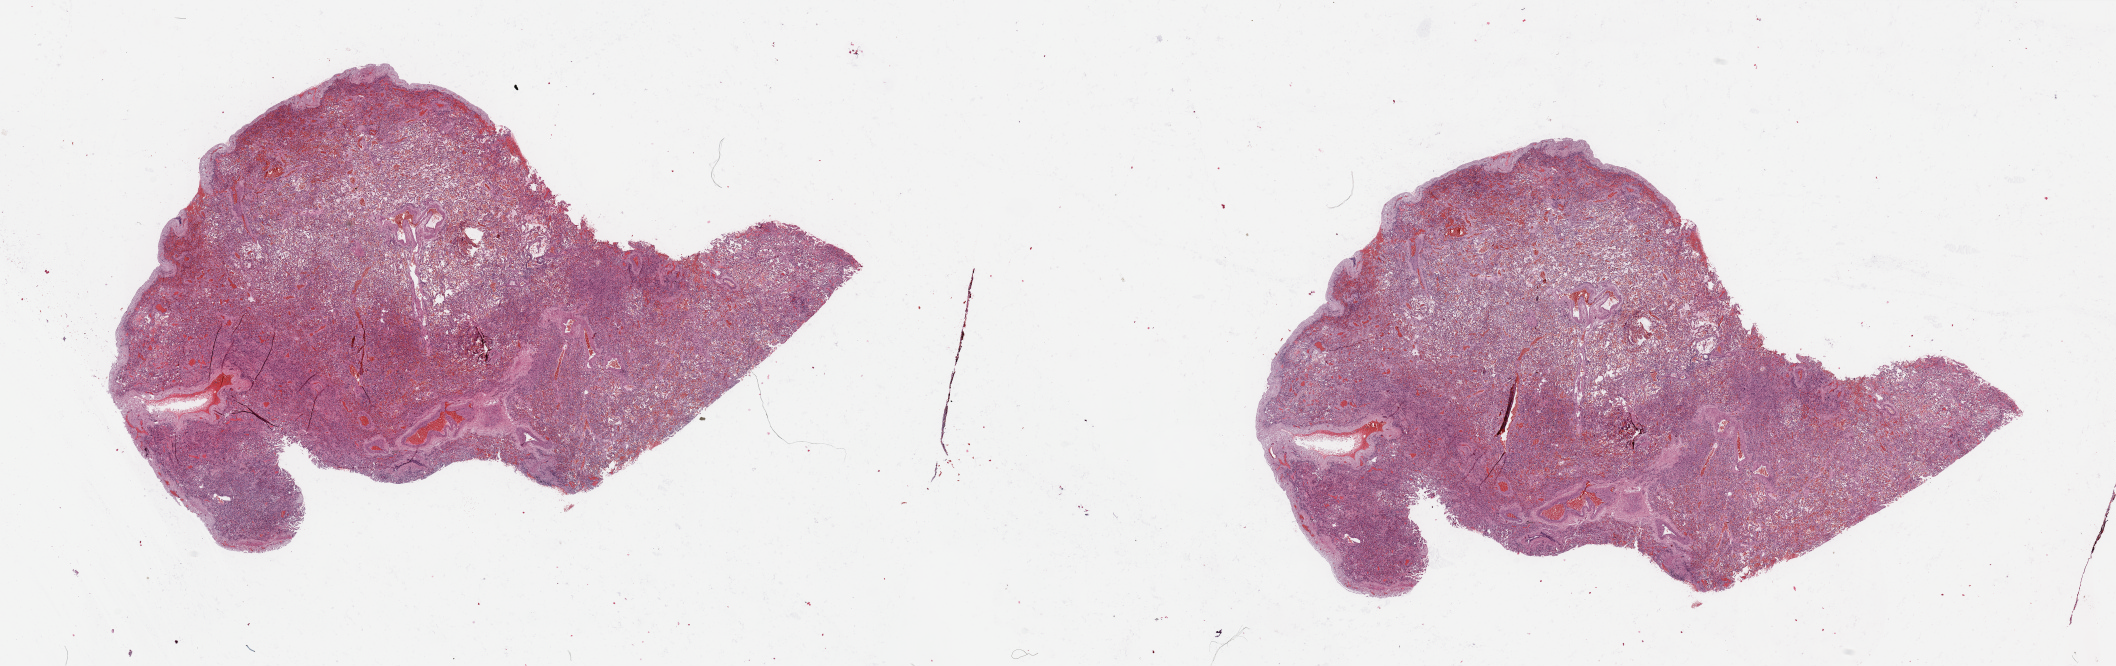
Whole-slide histology image, Hematoxylin and eosin (H&E) stained — a low-resolution overview of the entire scanned area, about 33.5 x 10.5 mm (slide scanned at 20x). Lung, normal (non-tumour) tissue. Patient: male, age 54 years.
This section: normal (non-tumour) tissue from the same patient. Patient diagnosis: Squamous cell carcinoma, NOS.